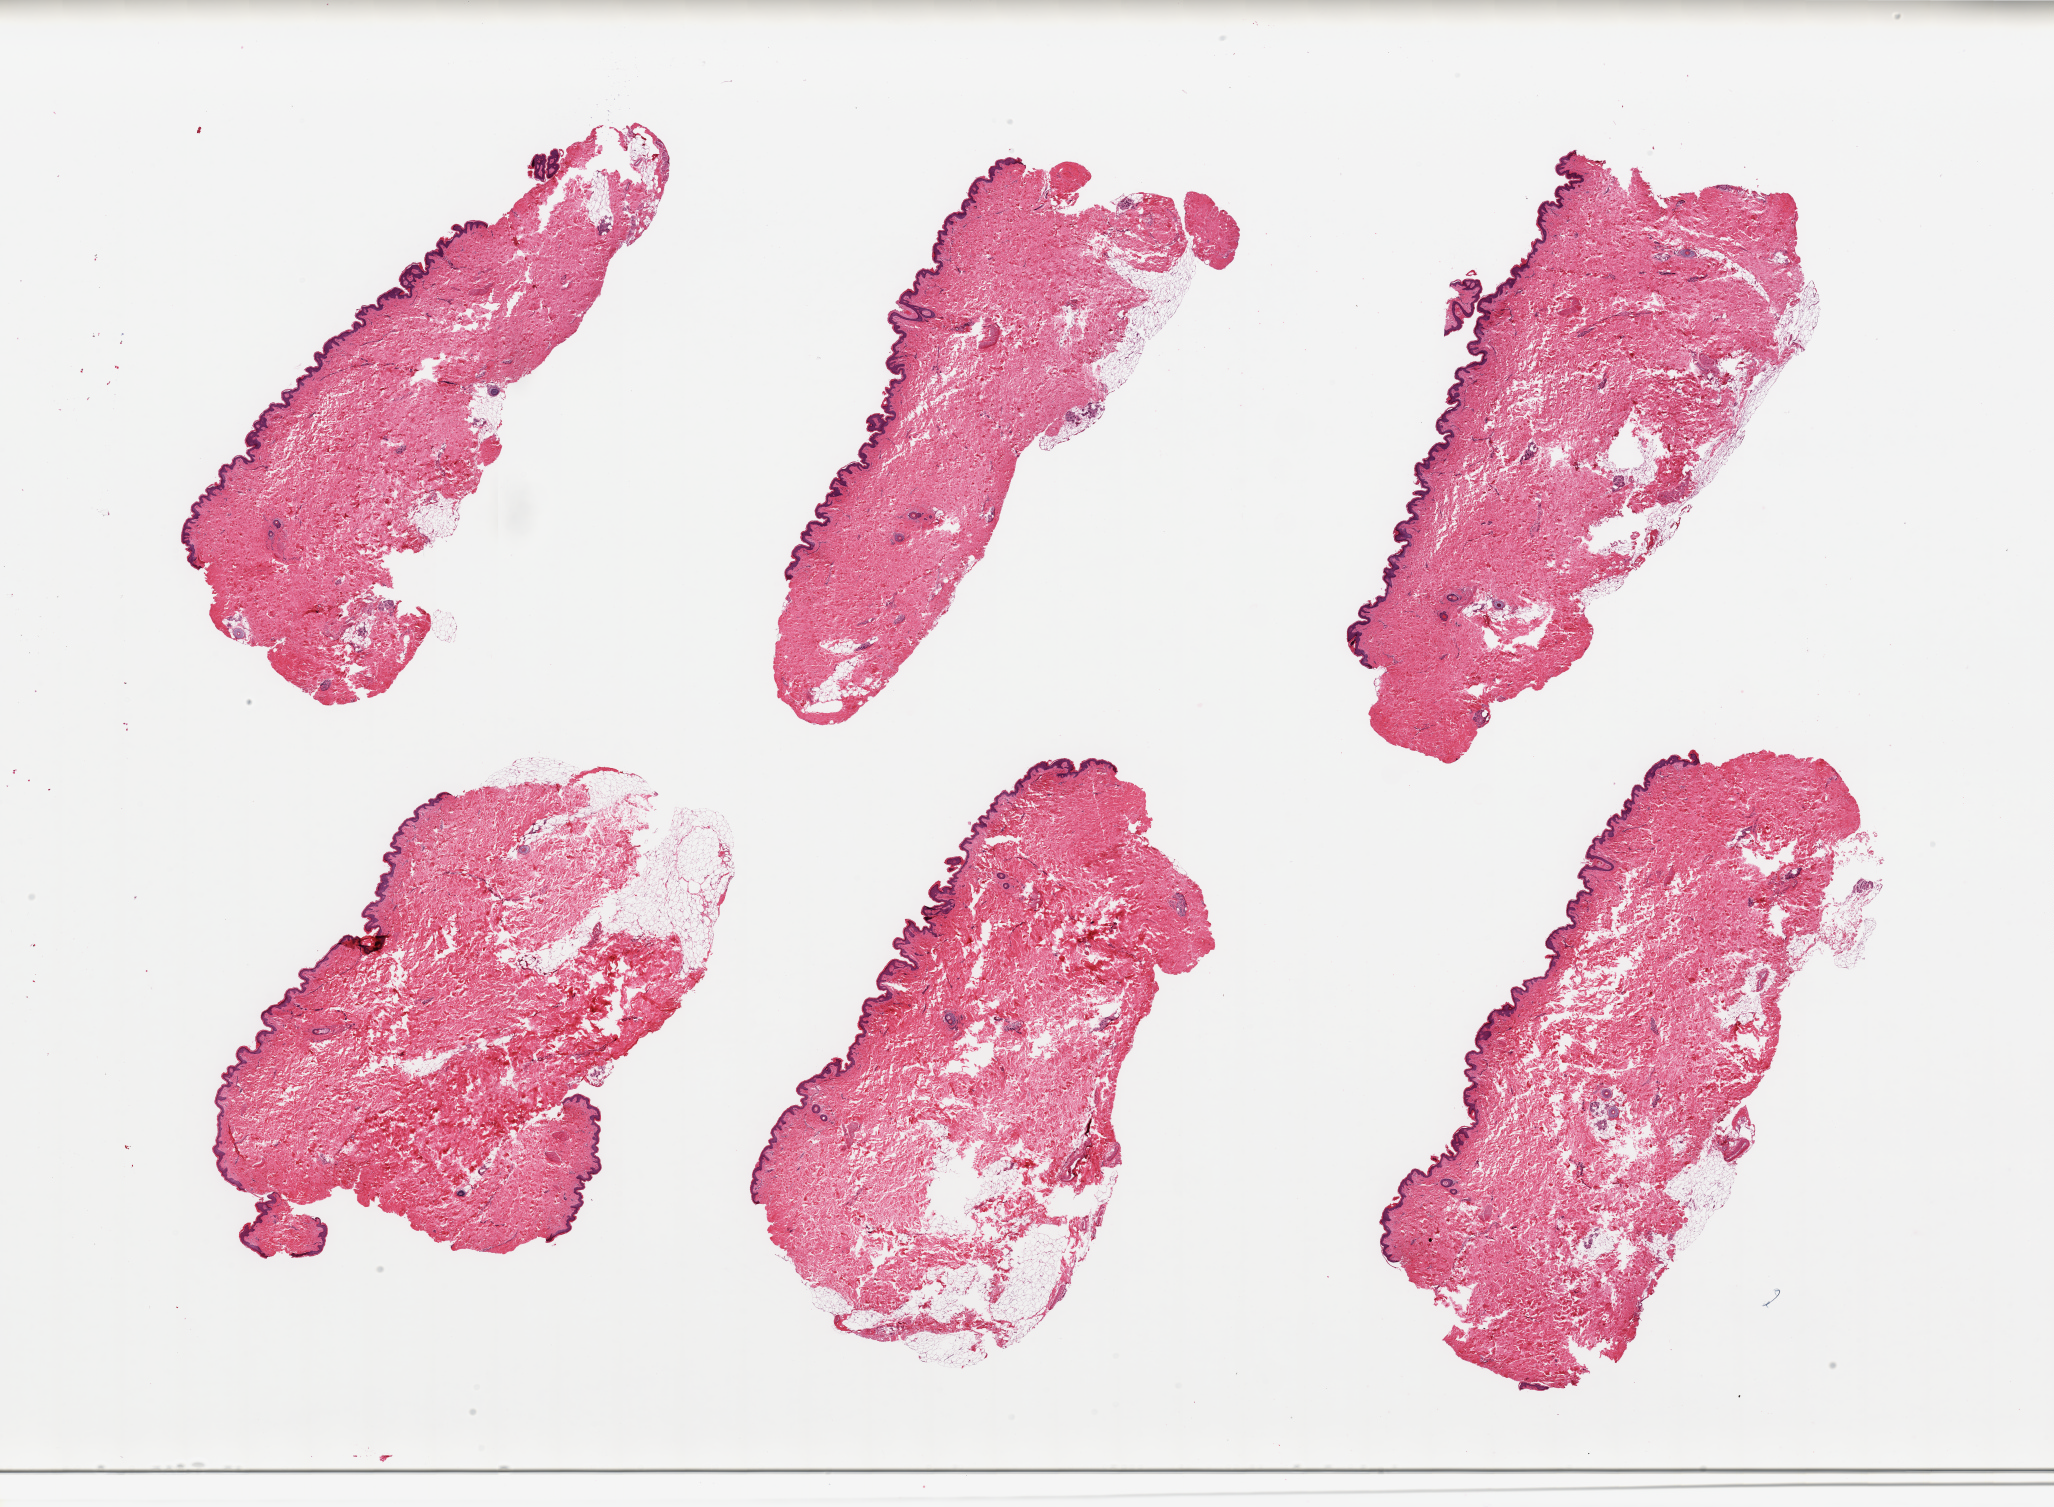
Haematoxylin and eosin whole-slide image, brightfield, shown as a low-resolution overview of the whole scanned area (about 32.5 x 23.8 mm). PAXgene-fixed paraffin-embedded (PFPE) section. Sampled site (target tissue): skin of suprapubic region. Tissue donor sample. Donor: female.
Review note (as recorded): 6 pieces, mild/moderate dermal fat; squamous epithelium is ~50-60 microns.